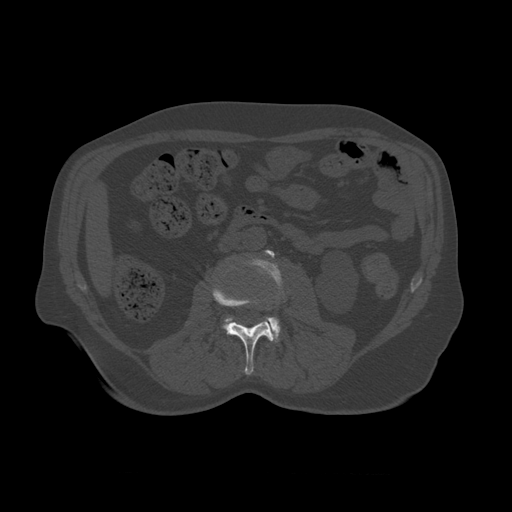
CT including the spine, one axial slice. Position 321 of 450 along the scan axis. Reconstruction kernel STANDARD. 120 kVp. Bone window (W 1800 / L 400 HU). 1.25 mm slice thickness. 512 × 512 image matrix, field of view 405 × 405 mm. Patient age 75 years. From the clinical record (not read from this slice): primary cancer: prostate.
Structures marked on this image (semi-automatic segmentation, software-assisted and operator-edited):
- L2 vertebra: bounding box <212,281,282,376> (left, top, right, bottom; pixels)
- L3 vertebra: <225,250,284,343>